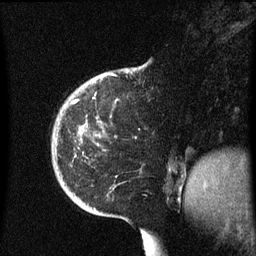
Breast MRI (dynamic contrast-enhanced), one sagittal slice; position 14 of 60 along the scan axis; dynamic contrast-enhanced series, image 2 of 3 at this slice position (ordered by acquisition); 1.5 T; TE 4.2 ms, TR 8.4 ms; 256 × 256 image matrix. Female patient, age 38 years. From the clinical record (not read from this slice): setting: breast cancer imaged before/during neoadjuvant chemotherapy; receptor status: HER2-positive.
Outlined on this slice (semi-automatic segmentation, software-assisted and operator-edited):
- analysis volume of interest (the breast-tissue region the enhancement analysis was run in; not a lesion): bounding box [x1, y1, x2, y2] px = [52, 78, 118, 213]
- tumour enhancement mask (voxels above the 70 % enhancement threshold inside the analysis volume of interest): [72, 100, 78, 103]